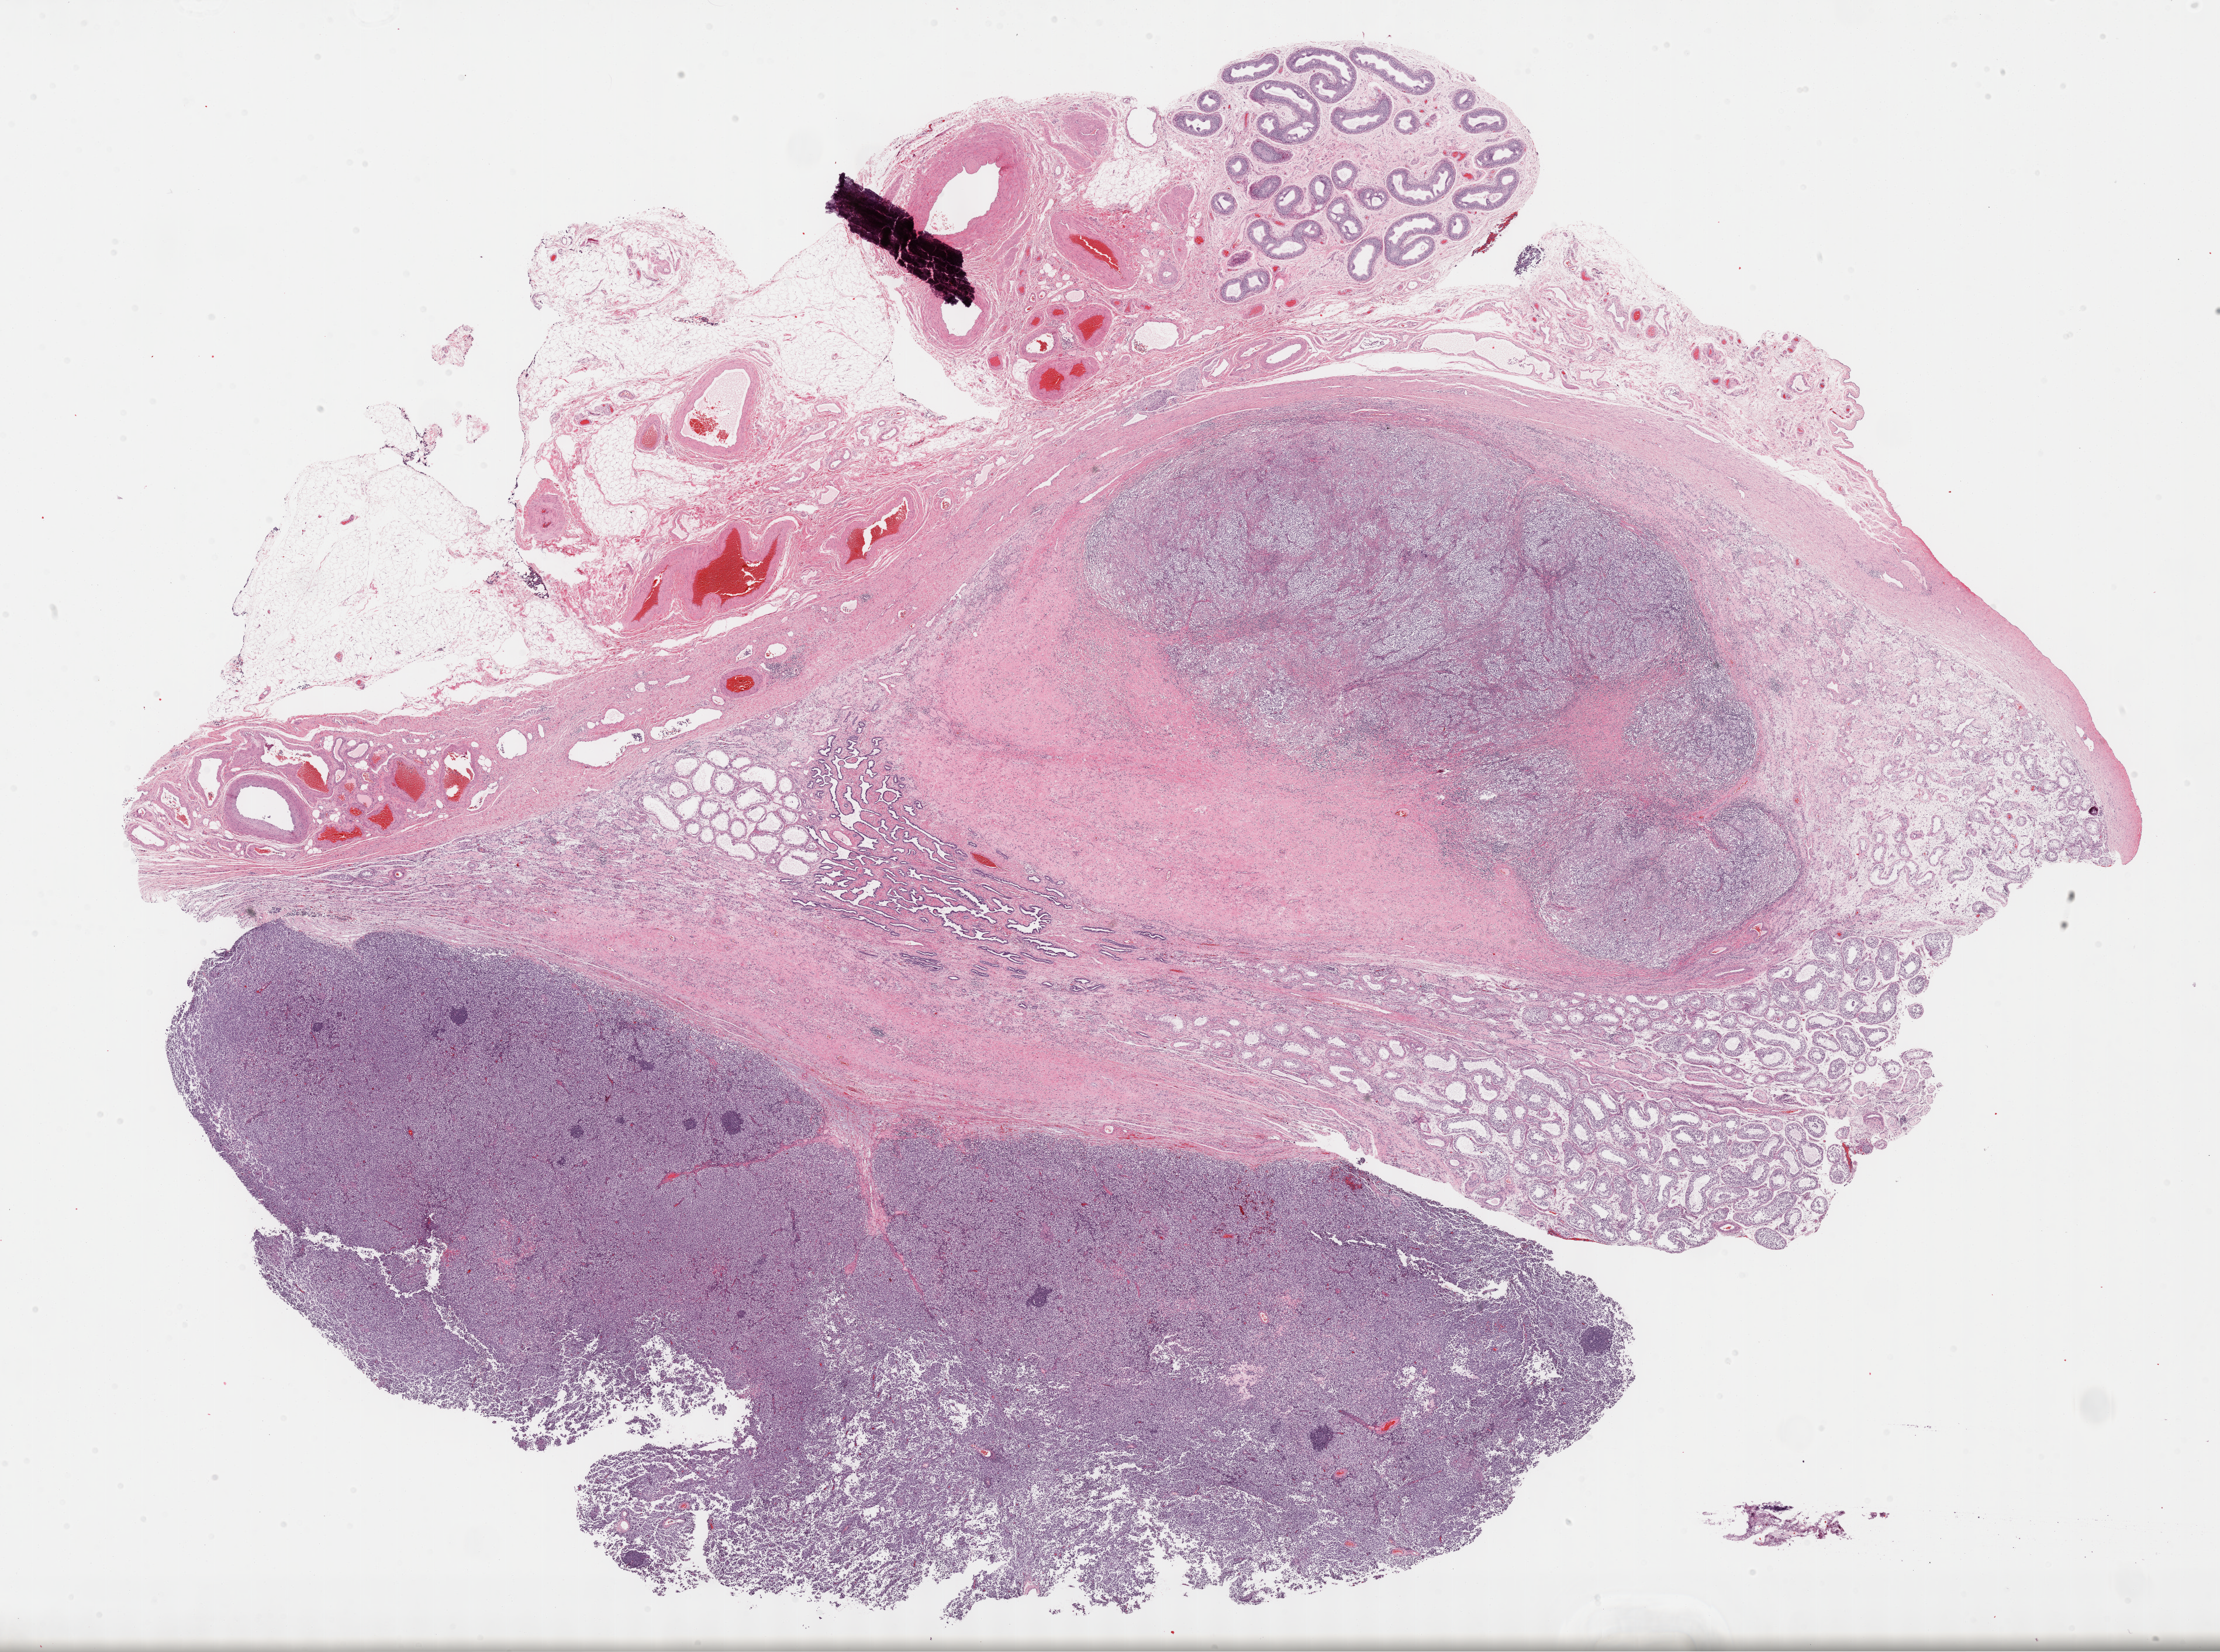
Digitized Hematoxylin and eosin (H&E) stained tissue section (whole slide) — whole scanned area (about 30.7 x 22.9 mm) shown as a low-resolution overview, formalin-fixed paraffin-embedded (FFPE) diagnostic section, primary tumour sample from the testis. Male, age 37 years at initial diagnosis.
Diagnosis: Seminoma, NOS.